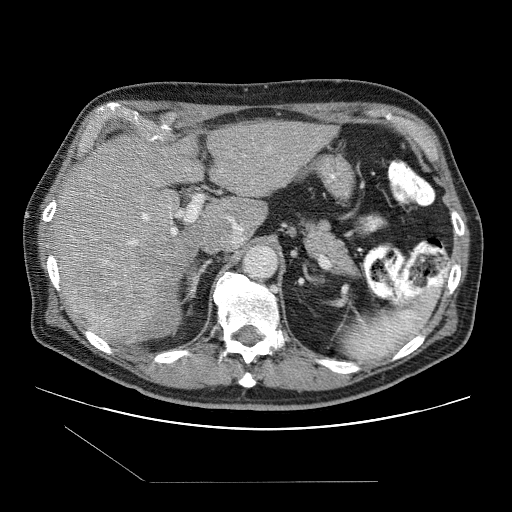
Contrast-enhanced abdominal CT (liver protocol), one axial slice; position 63 of 109 along the scan axis; one of 2 acquisitions stored at this slice position; soft-tissue window (W 400 / L 40 HU); 512 × 512 image matrix. Case-level facts recorded for this patient, not image findings: diagnosis: hepatocellular carcinoma (patient treated with transarterial chemoembolisation; whether this scan precedes or follows treatment is not stated here); TNM stage (as recorded): Stage-IIIB; Child-Pugh class: A; tumour differentiation: well differentiated.
Annotated regions visible in this slice (semi-automatically segmented with operator editing):
- liver parenchyma outside the tumour (the mass and vessels are separate outlines, so this box may not span the whole liver): bounding box [x1, y1, x2, y2] px = [53, 120, 336, 340]
- mass: [66, 252, 163, 335]
- liver vessels: [127, 213, 235, 245]